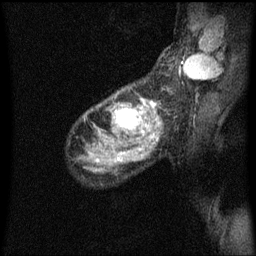
Breast MRI (dynamic contrast-enhanced), one sagittal slice; dynamic contrast-enhanced series, image 2 of 3 at this slice position (ordered by acquisition); 1.5 T; TE 4.2 ms, TR 8.4 ms; 2 mm slice thickness; 256 × 256 image matrix, field of view 200 × 200 mm. Female patient, age 49 years.
Annotated regions visible in this slice (semi-automatically segmented with operator editing):
- analysis volume of interest (the breast-tissue region the enhancement analysis was run in; not a lesion): bounding box [x1, y1, x2, y2] px = [103, 90, 157, 151]
- tumour enhancement mask (voxels above the 70 % enhancement threshold inside the analysis volume of interest): [116, 100, 157, 133]